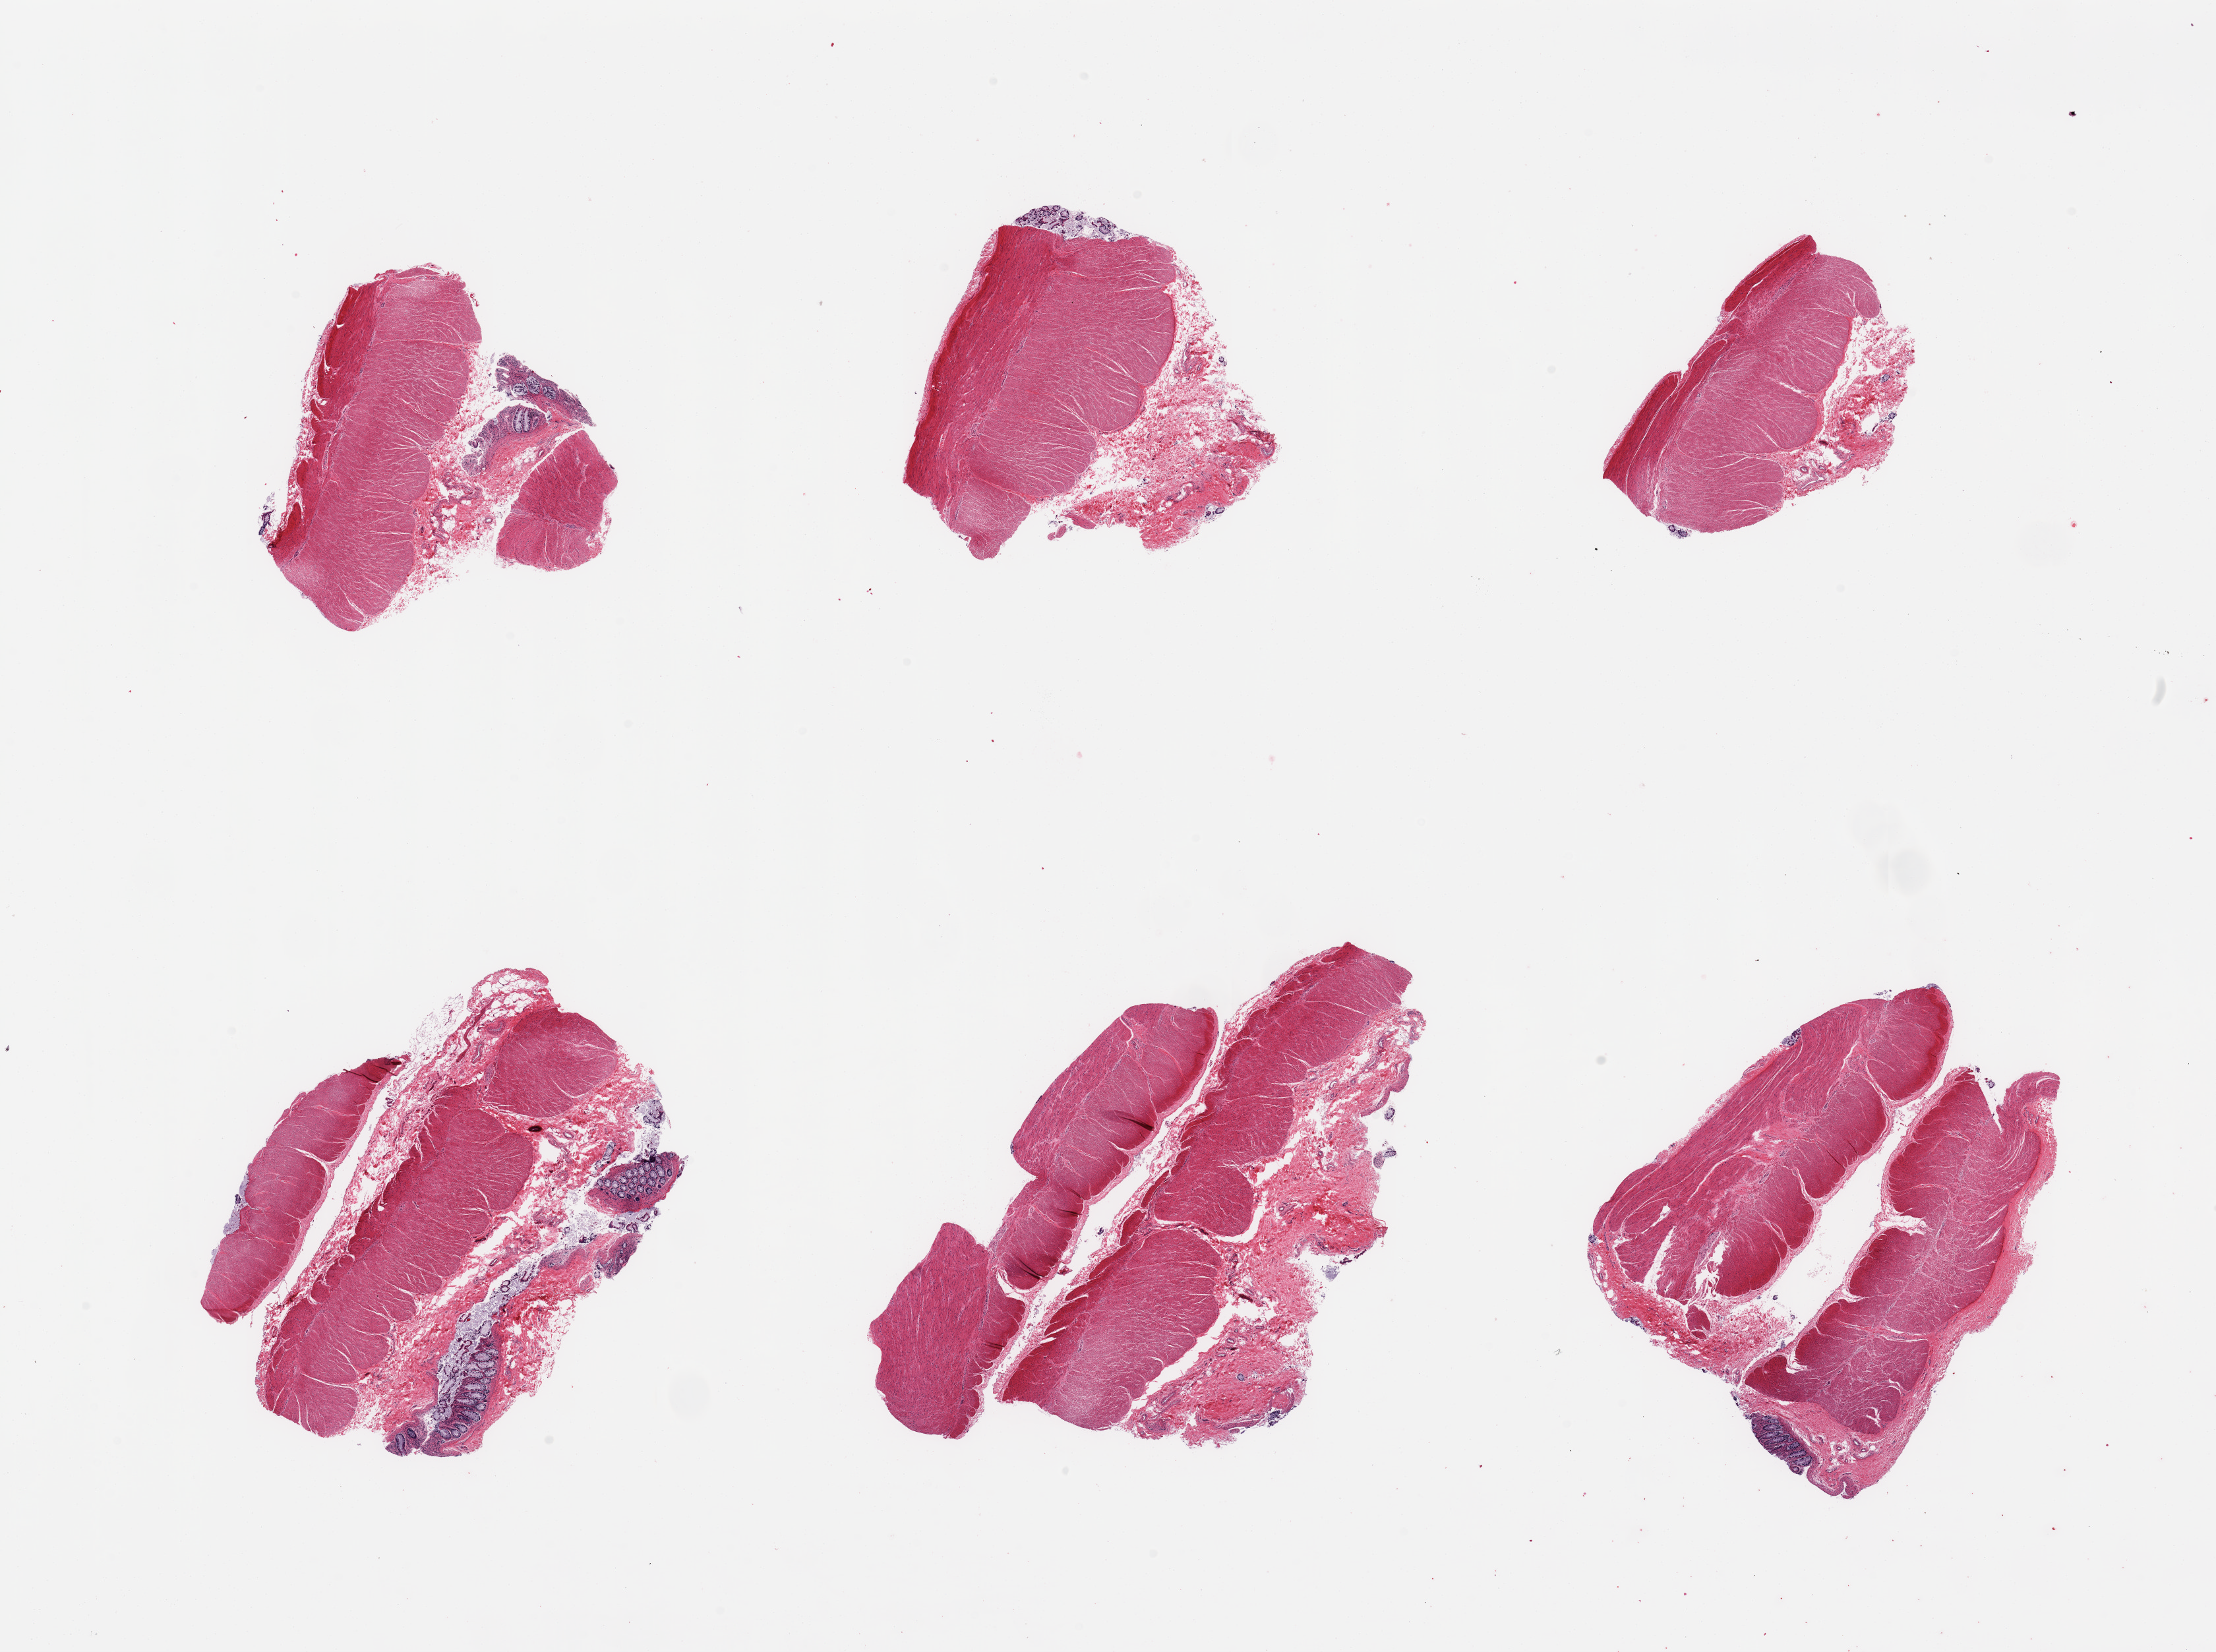
H&E whole-slide image, brightfield, a low-resolution overview of the entire scanned area, about 26.6 x 19.8 mm; PAXgene-fixed paraffin-embedded (PFPE) section; sampled site (target tissue): sigmoid colon; tissue donor sample. Male donor.
* reviewer comment on this tissue sample: 6 pieces; untrimmed mucosa comprises up to 10% of tissues